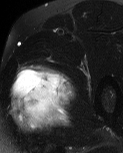
MRI of an extremity soft-tissue mass, one axial slice; position 41 of 60 along the scan axis; T2-weighted fat-saturated; MR volume resampled by the dataset authors to the PET/CT grid (not the native acquisition matrix); 3.27 mm slice thickness; 123 × 153 image matrix, field of view 120 × 149 mm. Male patient. From the clinical record (not read from this slice): histological type: pleiomorphic liposarcoma; grade: high; site of the primary tumour: left thigh.
Structures marked on this image (expert contour drawn on MRI and transferred to this co-registered scan by the dataset authors):
- gross tumour volume including surrounding oedema: bounding box <11,65,76,133> (left, top, right, bottom; pixels)
- gross tumour volume (mass): <13,70,67,117>